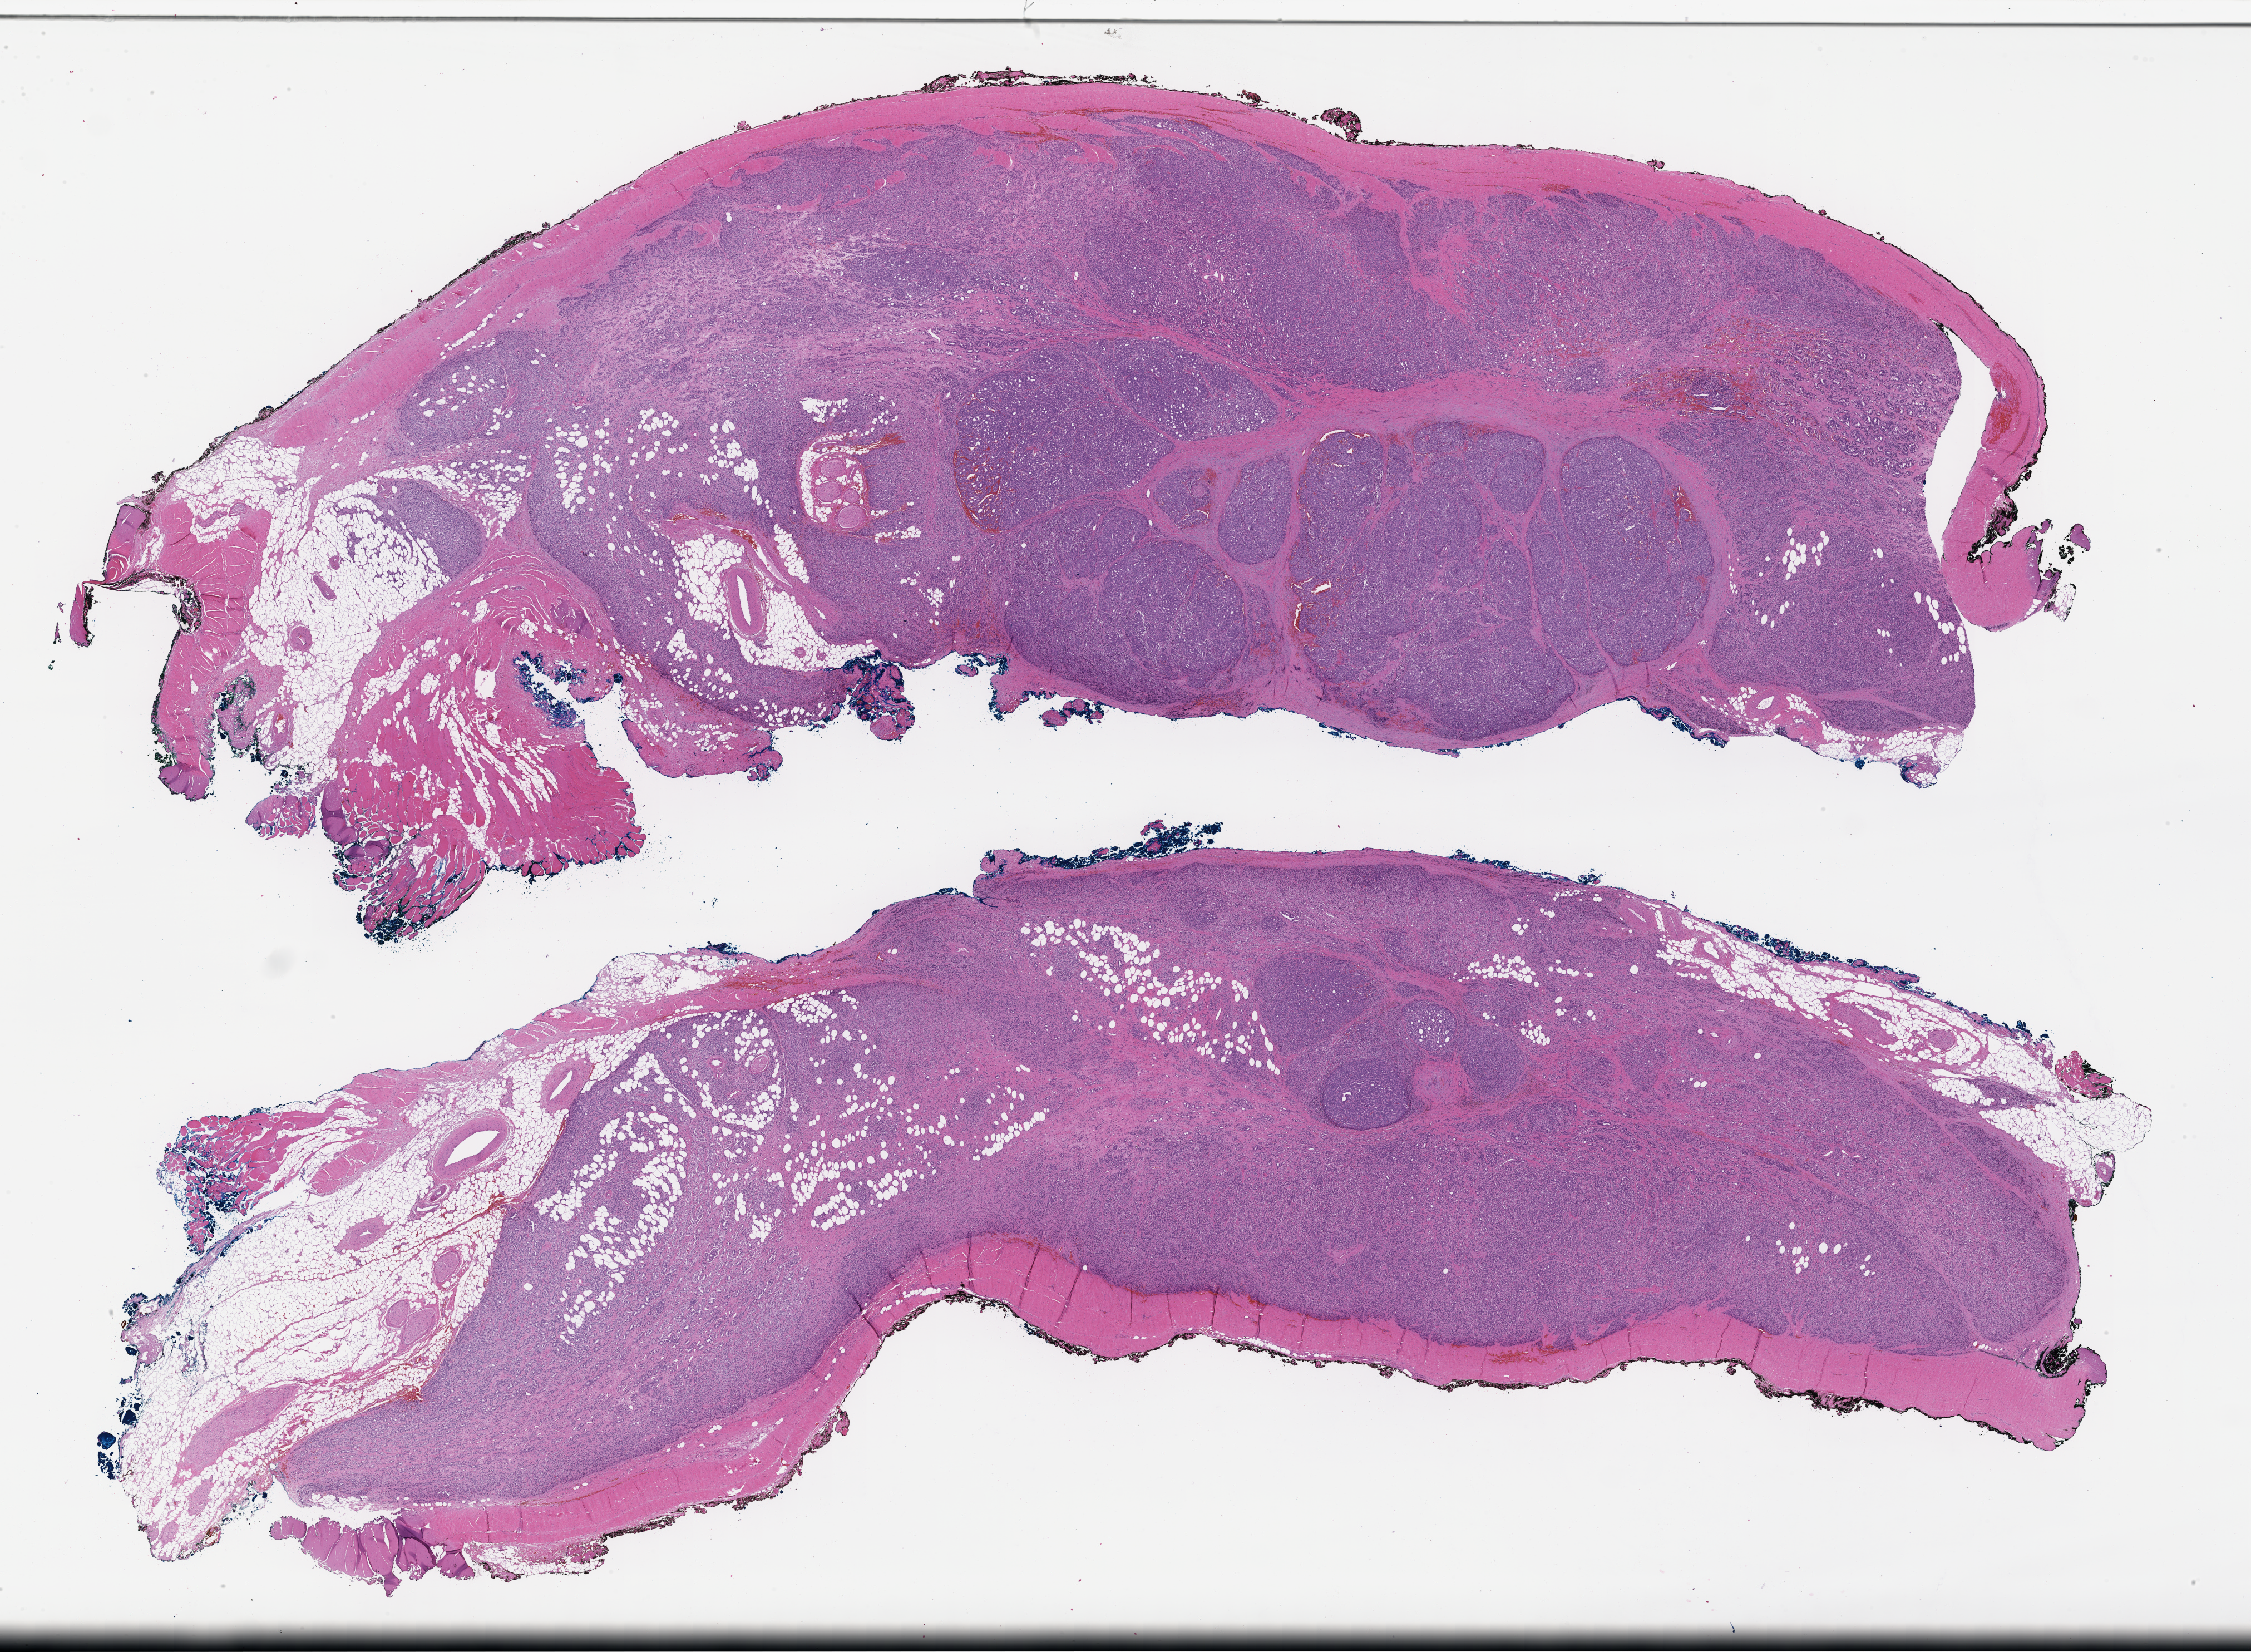
Whole-slide image, haematoxylin and eosin stain — low-resolution overview of the scanned area, about 32.7 x 24.0 mm. FFPE section. Specimen time point: archival tissue. Patient: male.
This section: metastatic tumor tissue. Primary diagnosis of the patient: Prostate Carcinoma.